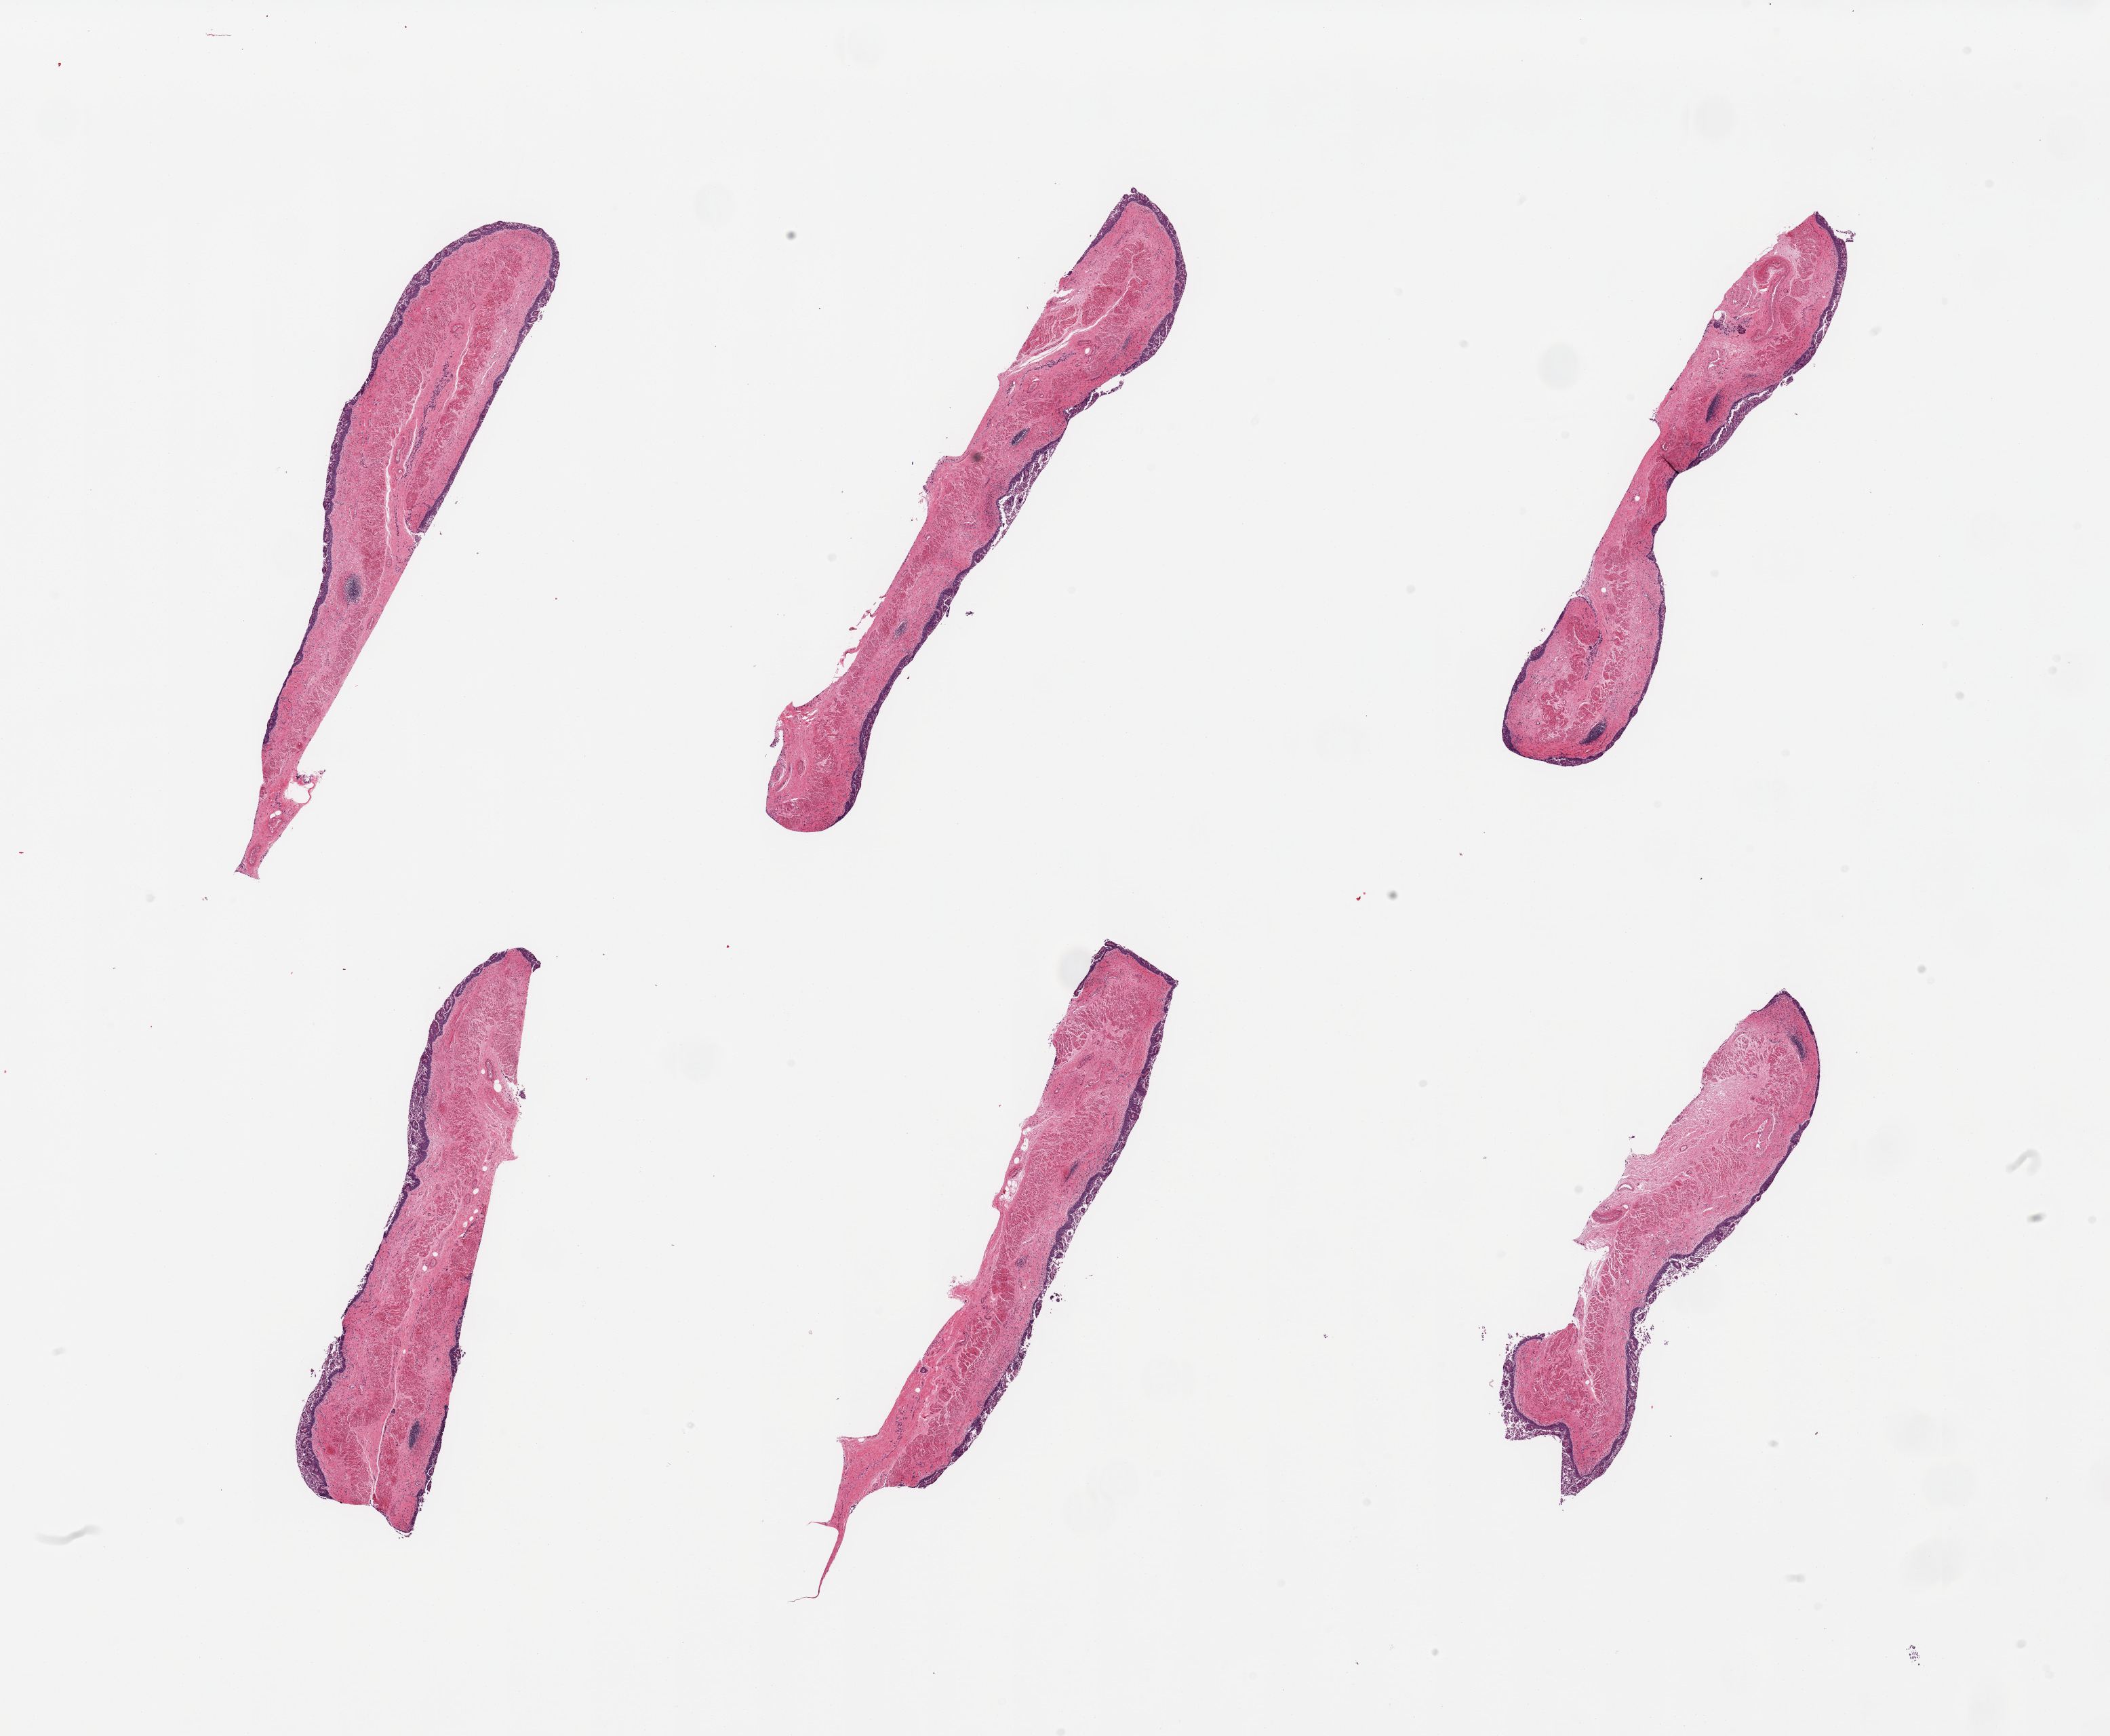
Digitized H&E-stained section, brightfield, a low-resolution overview of the entire scanned area, about 24.6 x 20.2 mm (slide scanned at 20x). PAXgene-fixed, paraffin-embedded tissue. Sampled site (target tissue): esophageal mucous membrane. Tissue donor sample.
* pathologist's review note for this sample: 6 pieces, squamous mucosa sloughing, residual up to ~150 microns